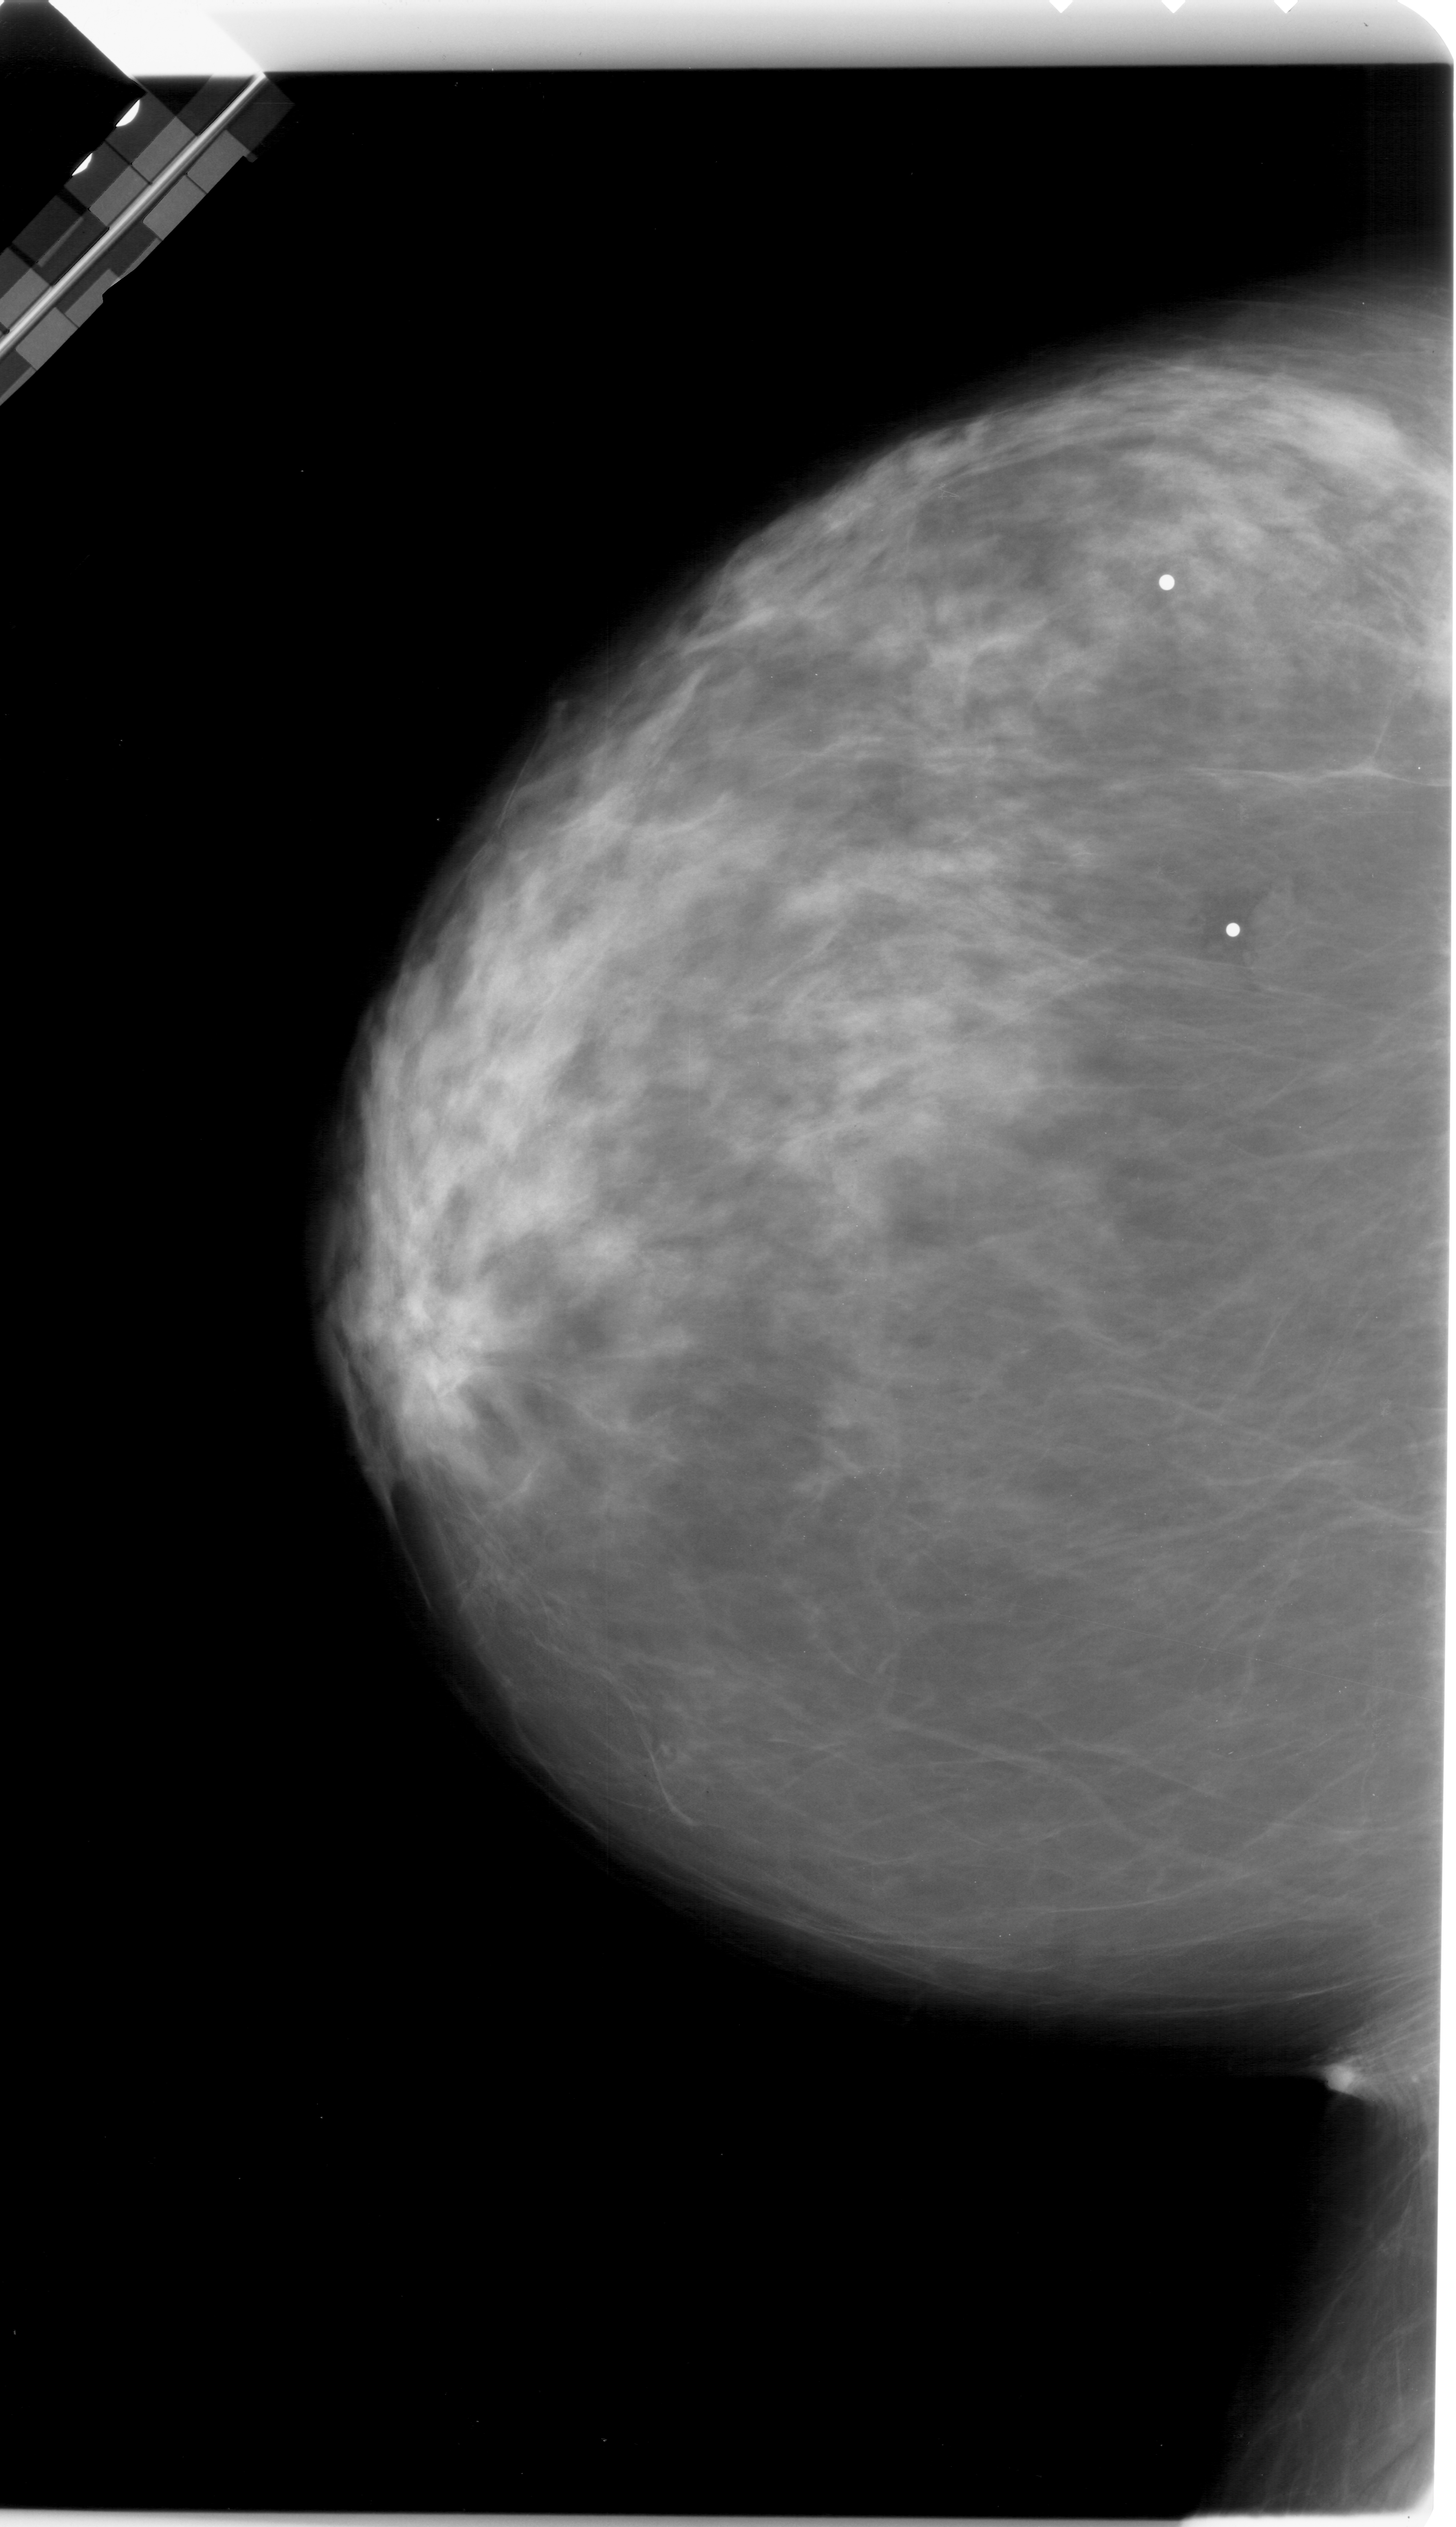
Digitized screen-film mammogram; left breast; craniocaudal (CC) view; breast composition: heterogeneously dense (BI-RADS density category 3 of 4); 1456 × 2527 image matrix.
Expert-marked regions of interest on this image (one box per marked abnormality):
- mass, shape lobulated, margins obscured; BI-RADS assessment category 4; pathology result (as recorded, not read from the image): malignant: box from (x=1304, y=389) to (x=1409, y=484) px